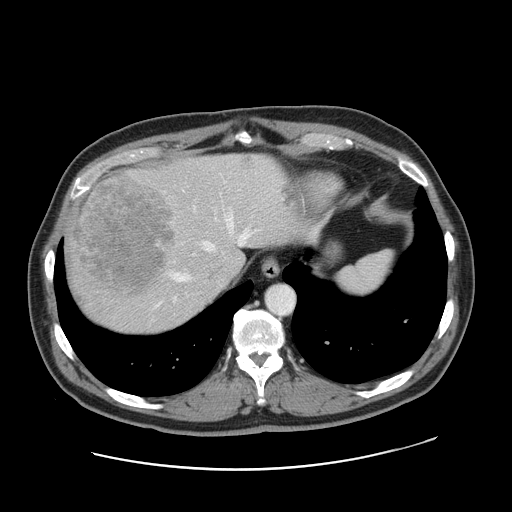
Contrast-enhanced abdominal CT, one axial slice. 120 kVp. Intravenous contrast given. Soft-tissue window (W 400 / L 40 HU). 512 × 512 image matrix, field of view 403 × 403 mm. Male patient, age 63 years. Case-level facts recorded for this patient, not image findings: diagnosis: colorectal cancer liver metastases, imaged before liver resection; multiple liver metastases: yes; largest metastasis: 8 cm; disease in both lobes: yes.
Annotated regions visible in this slice (expert manual segmentation):
- hepatic veins: bounding box <174,207,248,281> (left, top, right, bottom; pixels)
- liver: <65,154,299,333>
- planned liver remnant (the part of the liver to remain after resection): <161,156,299,281>
- portal vein (with intrahepatic branches): <157,242,159,245>
- liver metastasis: <243,158,252,167>
- liver metastasis: <68,176,176,297>